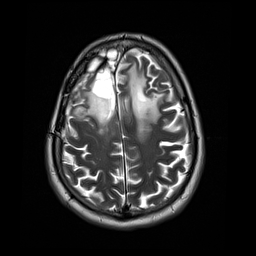
Brain MRI from a brain-tumour surgery series, one axial slice. Slice 12 of 44 in the series (ordered by position). 4 mm slice thickness. 256 × 256 image matrix. From the clinical record (not read from this slice): histopathology: Astrocytoma; WHO grade: 4; IDH mutation: yes.
Structures marked on this image (manually delineated by an expert):
- tumour: box from (x=72, y=92) to (x=112, y=135) px